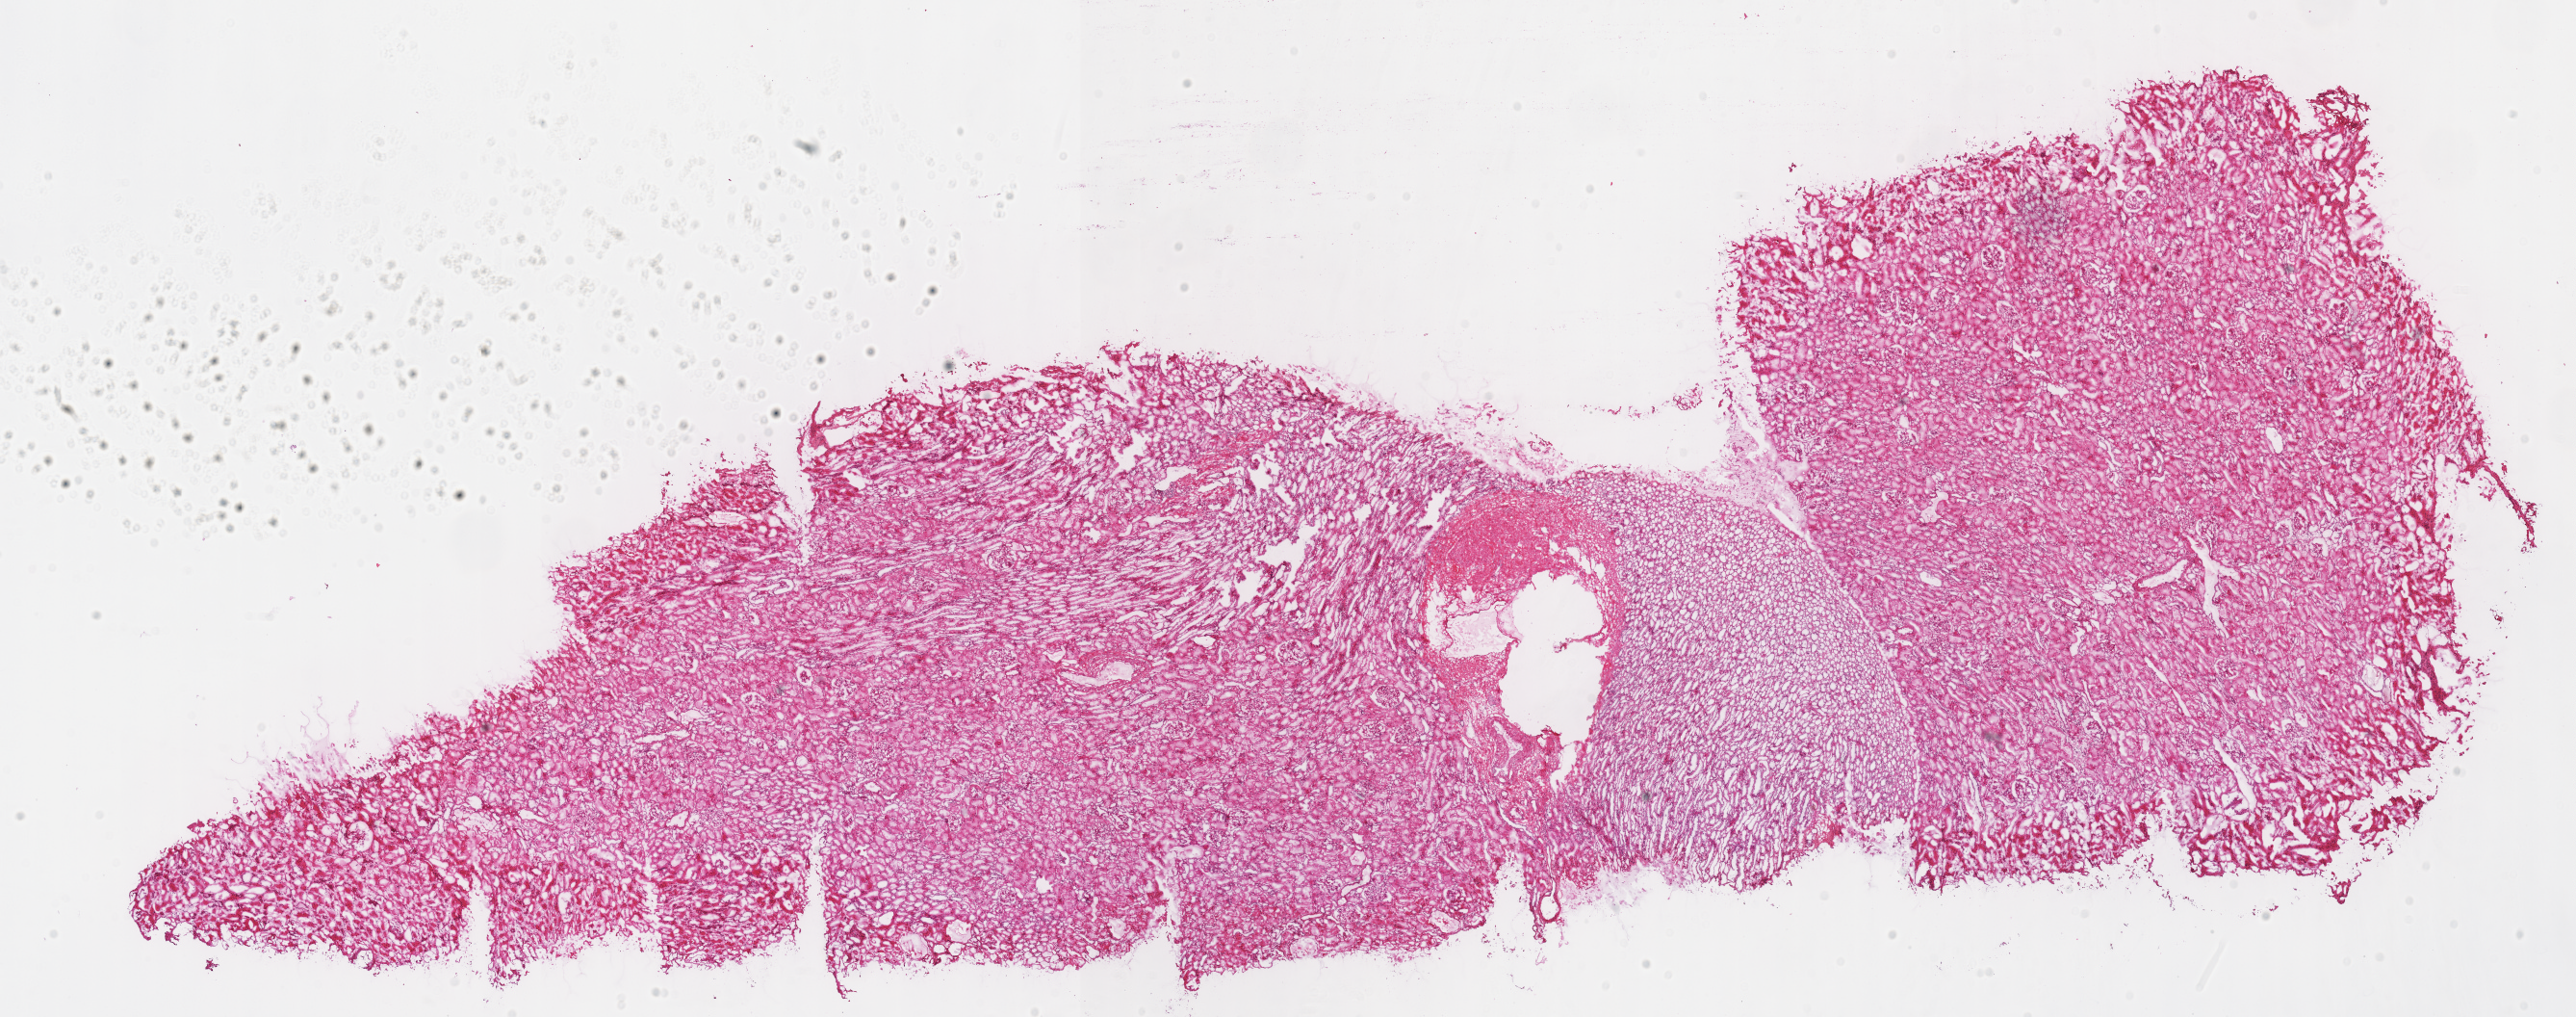
Digitized H&E tissue section (whole slide), low-resolution overview of the scanned area, about 21.0 x 8.3 mm (acquisition: 40x scan). Frozen section from the top of the tissue portion. Sample: solid tissue normal (non-tumour tissue), kidney. Patient: male, age at initial diagnosis 41 years.
This section: solid tissue normal sample (biorepository sample class). Patient diagnosis: Renal cell carcinoma, chromophobe type.